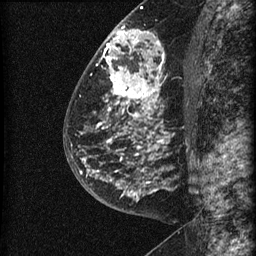
Breast MRI (dynamic contrast-enhanced), one sagittal slice. Slice 34 of 60 in the series (ordered by position). Dynamic contrast-enhanced series, image 2 of 3 at this slice position (ordered by acquisition). 1.5 T. TE 4.2 ms, TR 22.7 ms. 256 × 256 image matrix, field of view 180 × 180 mm. Female patient, age 48 years. From the clinical record (not read from this slice): setting: breast cancer imaged before/during neoadjuvant chemotherapy; receptor status: triple-negative.
Annotated regions visible in this slice (semi-automatic segmentation, software-assisted and operator-edited):
- analysis volume of interest (the breast-tissue region the enhancement analysis was run in; not a lesion): bounding box <81,23,186,202> (left, top, right, bottom; pixels)
- tumour enhancement mask (voxels above the 90 % enhancement threshold inside the analysis volume of interest): <81,30,164,197>